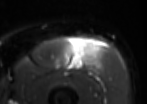
MRI of an extremity soft-tissue mass, one axial slice; T2-weighted fat-saturated; MR volume resampled by the dataset authors to the PET/CT grid (not the native acquisition matrix); 147 × 104 image matrix, field of view 144 × 102 mm. Male patient. From the clinical record (not read from this slice): histological type: extraskeletal osteosarcoma; grade: high; site of the primary tumour: thigh.
Structures marked on this image (expert contour drawn on MRI and transferred to this co-registered scan by the dataset authors):
- gross tumour volume (mass): bounding box (x1, y1, x2, y2) in pixels: (65, 40, 93, 70)